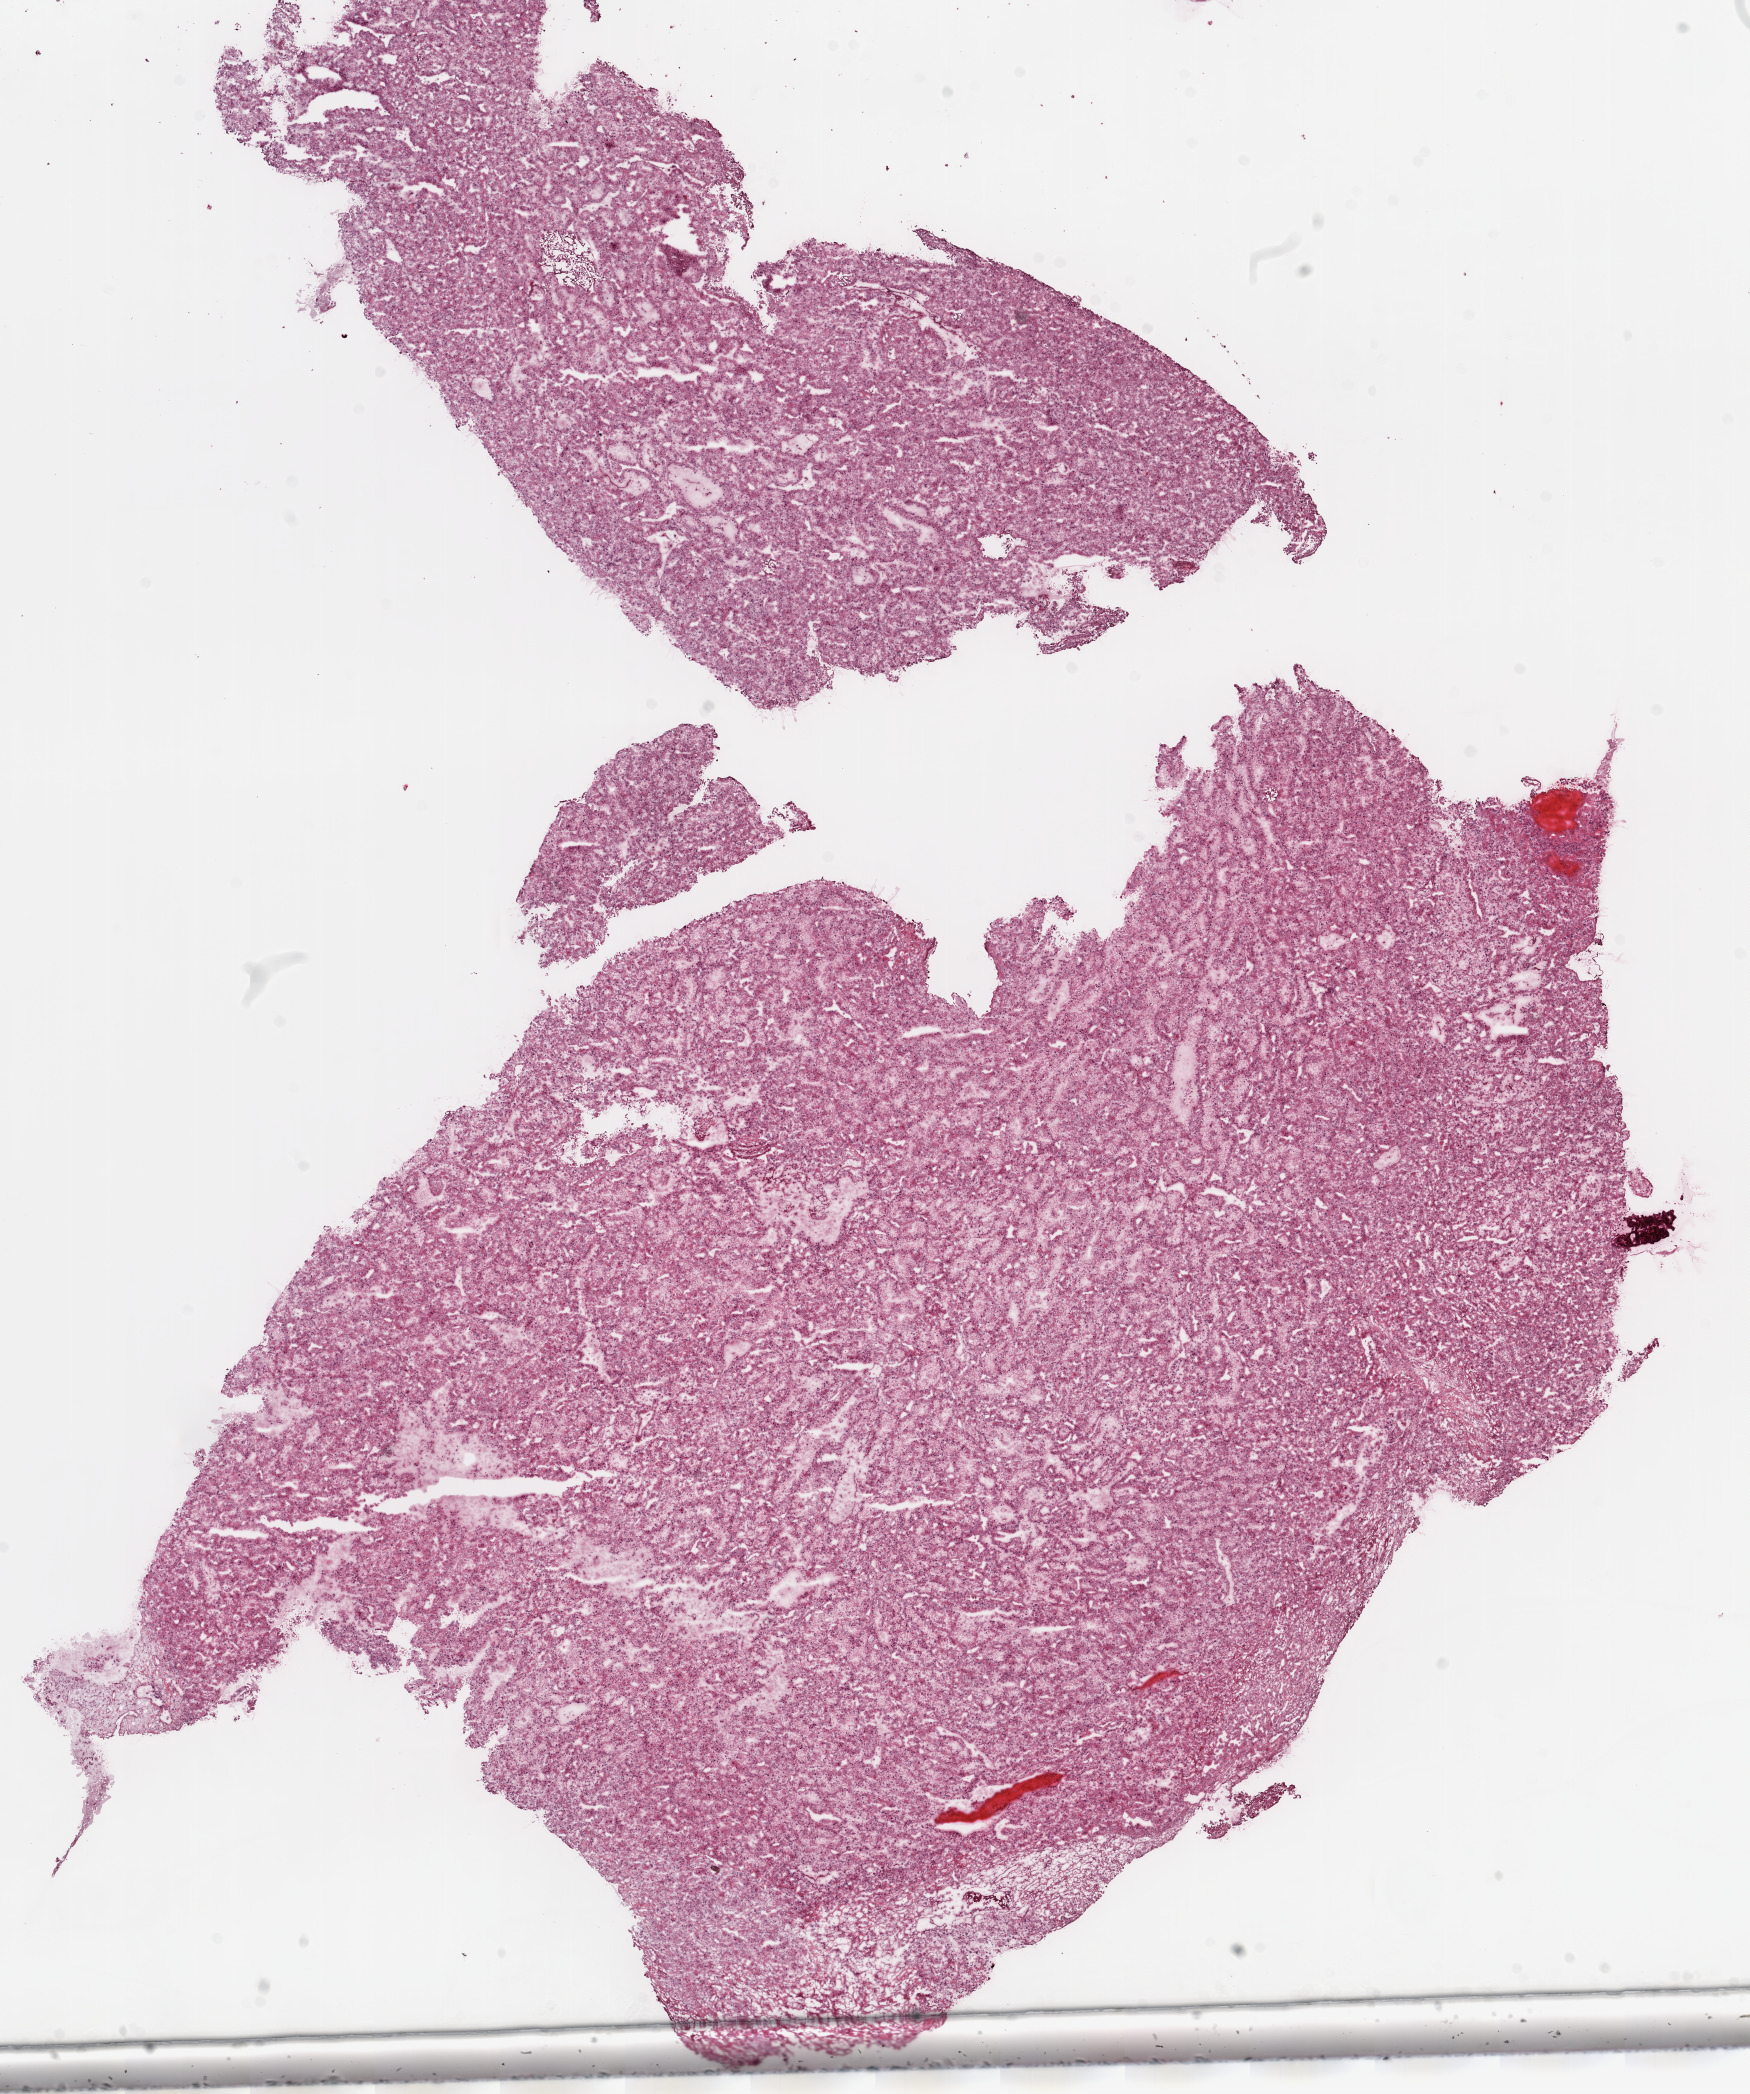
Digitized H&E tissue section (whole slide), shown as a low-resolution overview of the whole scanned area (about 14.0 x 16.8 mm, from a 20x scan). Frozen section. Kidney, primary tumour sample. Male, age 60 years at initial diagnosis. Histologic grade: G3 (poorly differentiated). Slide review estimates, as recorded: tumour cells 95%, tumour nuclei 90%, normal cells 0%, stromal cells 5%, necrosis 0%.
Pathologic diagnosis: Clear cell adenocarcinoma, NOS. Laterality: right. AJCC pathologic stage: I.